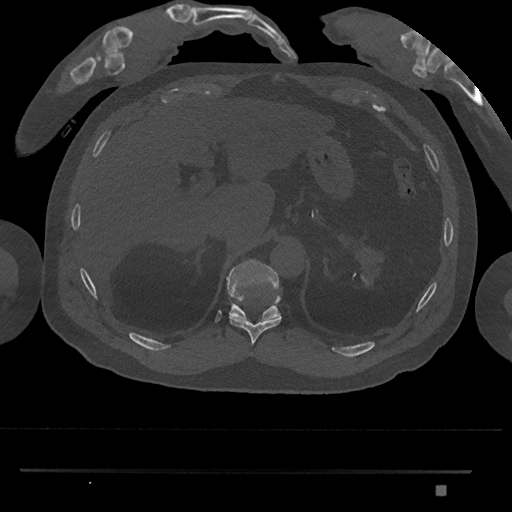
CT including the spine, one axial slice; position 979 of 1134 along the scan axis; 120 kVp; bone window (W 1800 / L 400 HU); 0.5 mm slice thickness; 512 × 512 image matrix. Patient: male, 65 years. Case-level facts recorded for this patient, not image findings: primary cancer: prostate.
Outlined on this slice (semi-automatic segmentation, software-assisted and operator-edited):
- T10 vertebra: box from (x=229, y=317) to (x=282, y=345) px
- T11 vertebra: (x=226, y=259)–(x=281, y=319)